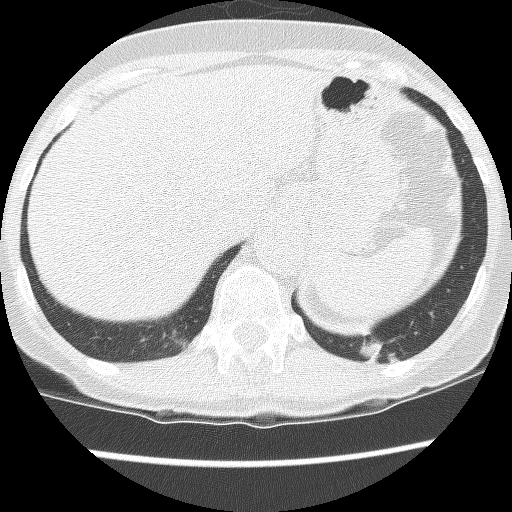
Low-dose screening chest CT, axial slice. Third annual screen. Lung window (W 1500 / L -600 HU). 2.5 mm slice thickness. Female participant, aged 61 years at enrolment. Current smoker at enrolment.
Expert-annotated lung lesion, box from (x=337, y=296) to (x=438, y=384) px. The screening reader recorded 2 non-calcified nodules or masses ≥4 mm on this exam (left lower lobe, left lower lobe); which of them this box marks is not recorded. Official screen result: positive, no significant change: stable abnormalities potentially related to lung cancer, unchanged since the prior screening exam. Later outcome: lung cancer diagnosed 166 days after this screen — non-small cell carcinoma, left lower lobe, poorly differentiated (G3), stage IB (AJCC 6th edition), 100 mm at pathology.